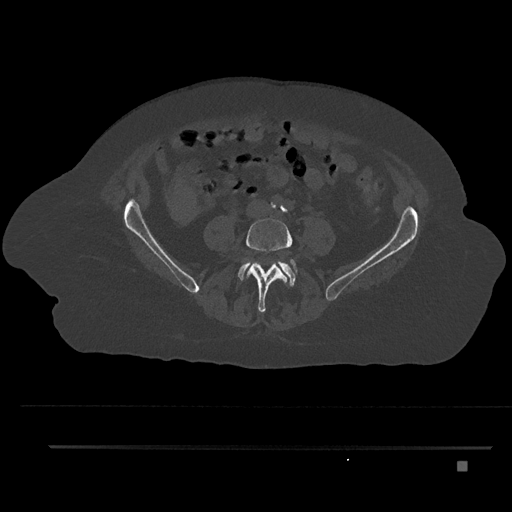
CT including the spine, one axial slice; position 71 of 797 along the scan axis; reconstruction kernel Br40s/3; 120 kVp; bone window (W 1800 / L 400 HU); 512 × 512 image matrix, field of view 437 × 437 mm. Female patient, age 76 years. From the clinical record (not read from this slice): primary cancer: lung.
Outlined on this slice (semi-automatically segmented with operator editing):
- L4 vertebra: bounding box <246,218,298,313> (left, top, right, bottom; pixels)
- L5 vertebra: <238,259,296,286>